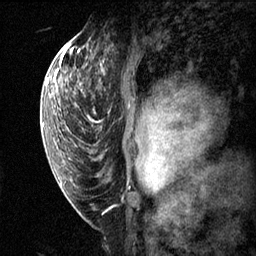
Breast MRI (dynamic contrast-enhanced), one sagittal slice. Slice 42 of 60 in the series (ordered by position). Dynamic contrast-enhanced series, image 2 of 3 at this slice position (ordered by acquisition). 1.5 T. TE 4.2 ms, TR 11.1 ms. 2 mm slice thickness. 256 × 256 image matrix, field of view 180 × 180 mm. Female patient, age 50 years.
Outlined on this slice (semi-automatically segmented with operator editing):
- analysis volume of interest (the breast-tissue region the enhancement analysis was run in; not a lesion): bounding box (x1, y1, x2, y2) in pixels: (82, 56, 163, 143)
- tumour enhancement mask (voxels above the 70 % enhancement threshold inside the analysis volume of interest): (141, 116, 163, 143)